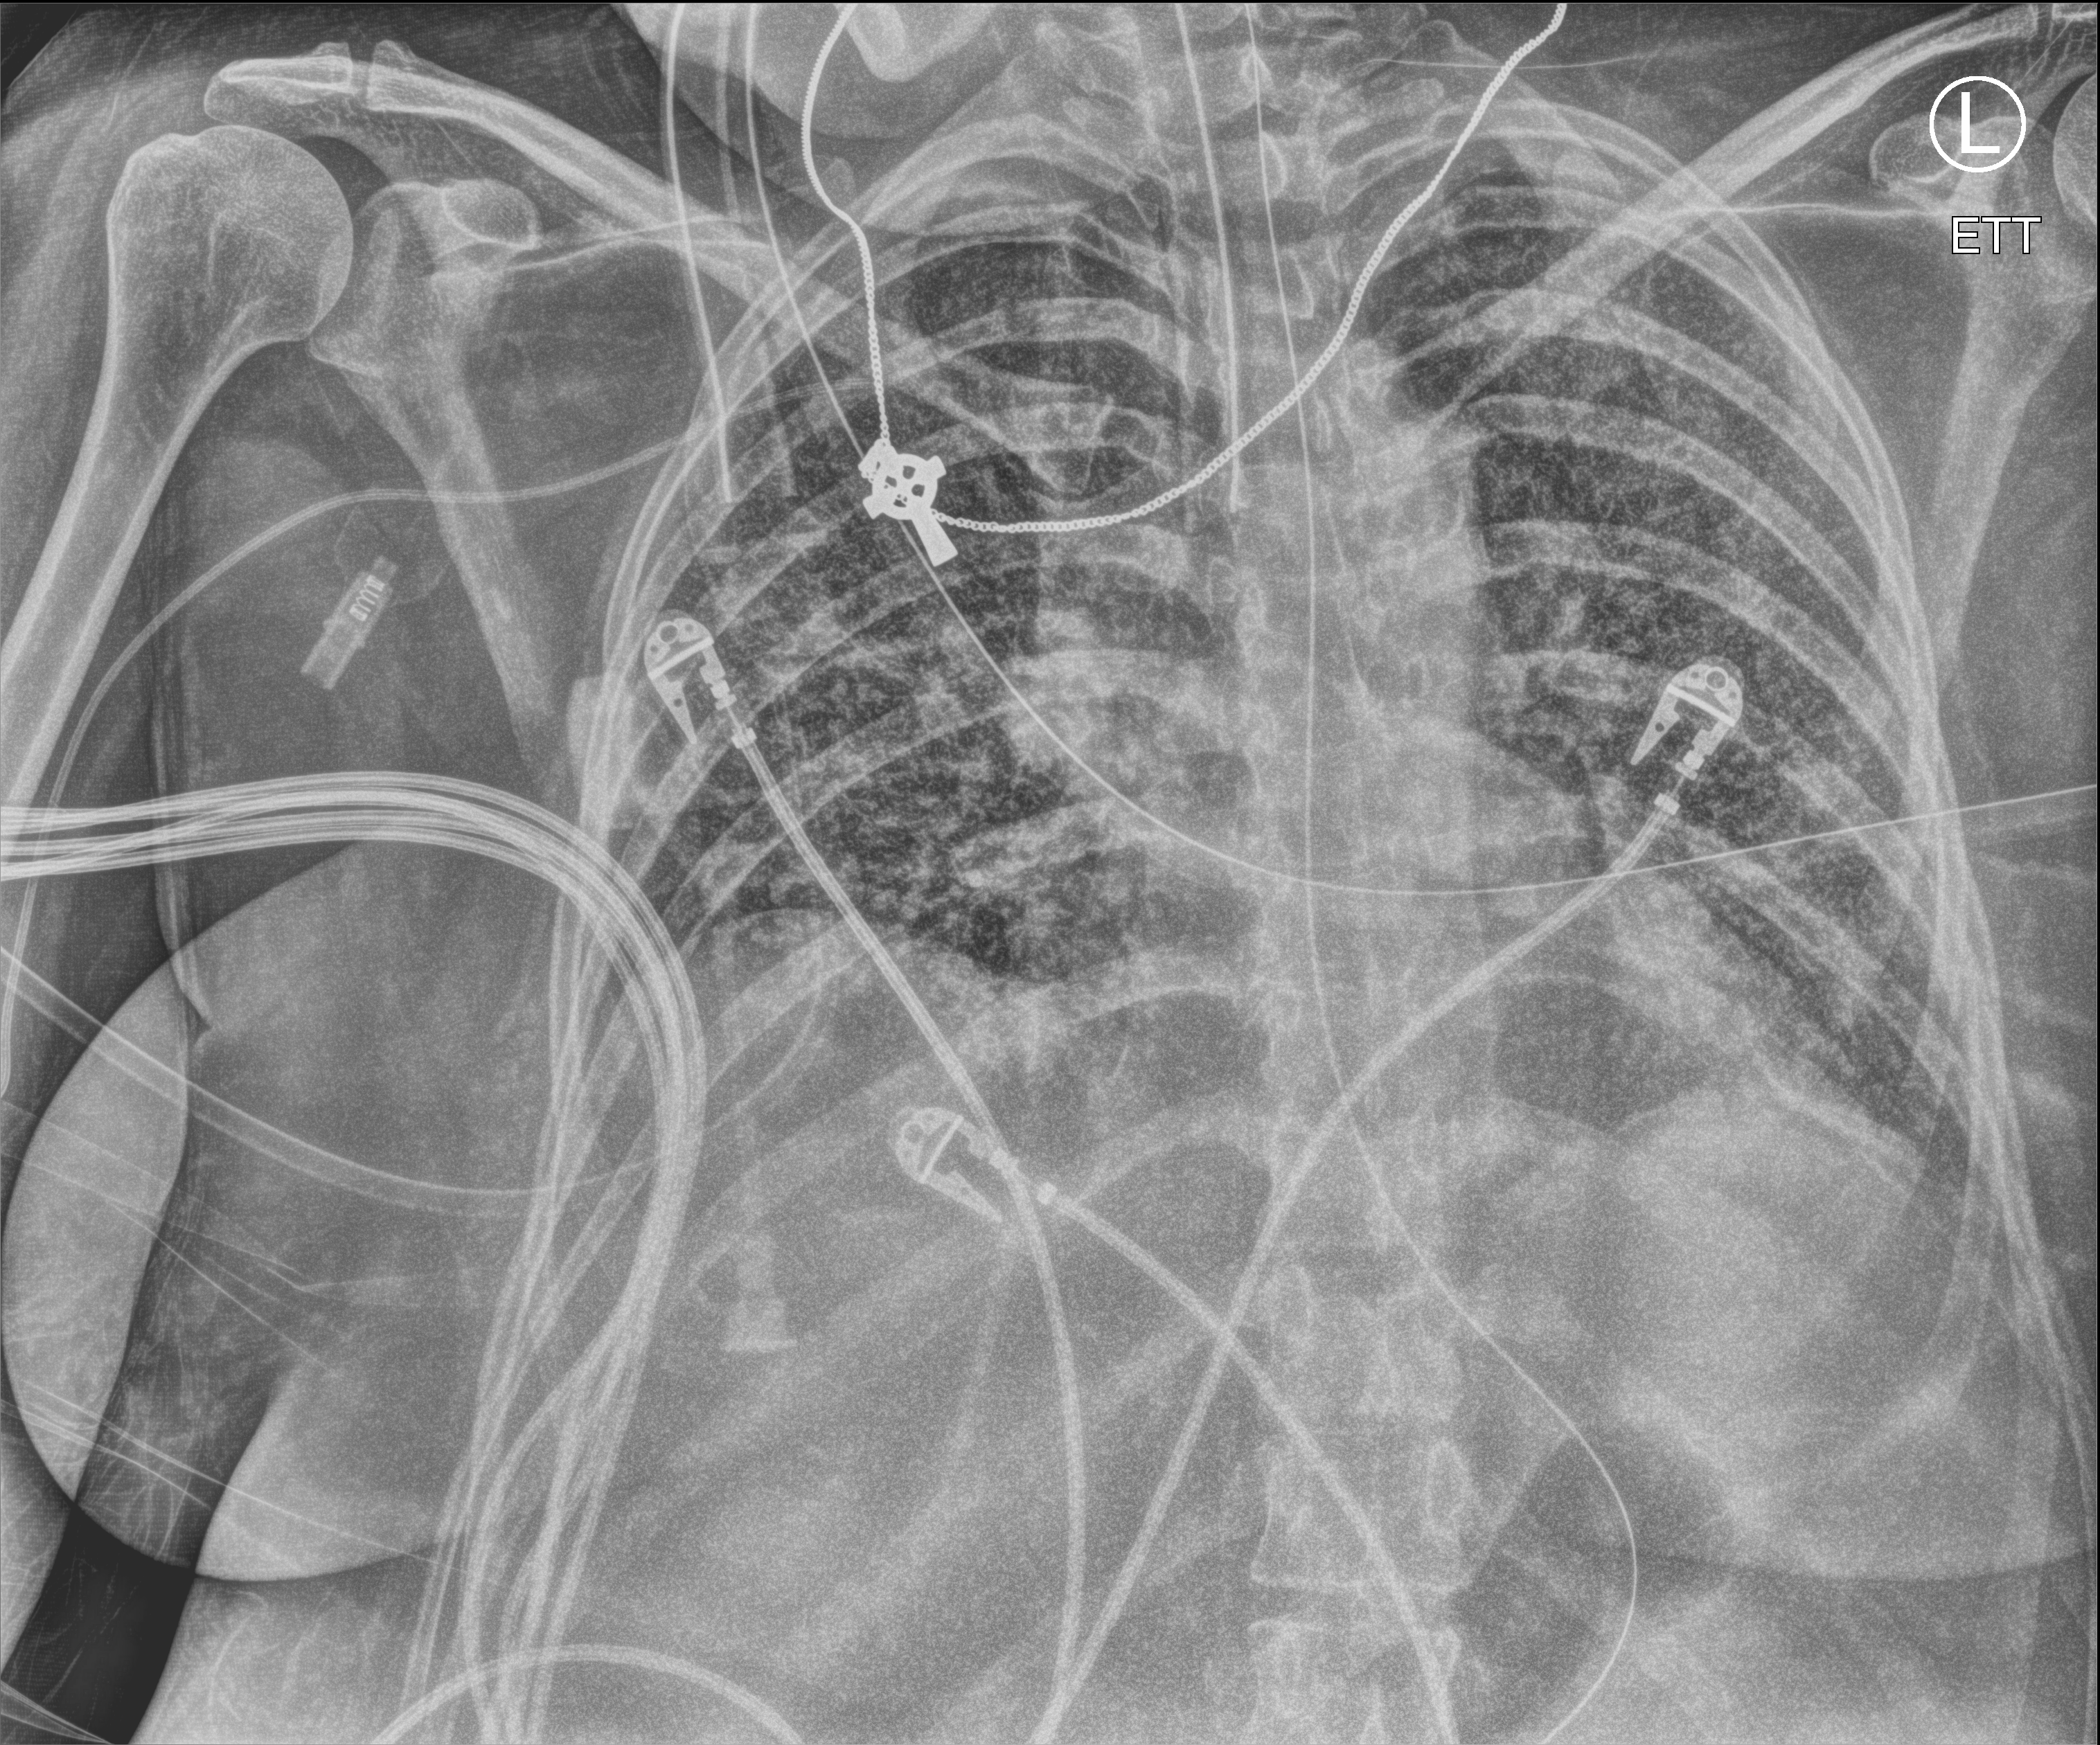
Portable chest radiograph; anteroposterior (AP) projection. Patient hospitalised with COVID-19; female, aged 18–59 years.
Admission-level facts for this patient (not findings on this image; timing relative to this image not recorded): mechanically ventilated during this hospital stay: yes.